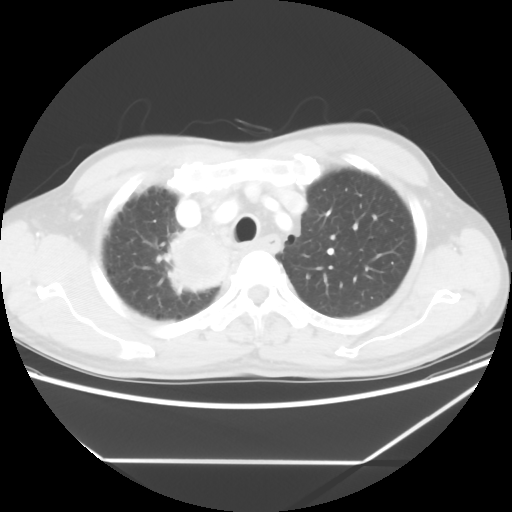
Chest CT, one axial slice; position 49 of 60 along the scan axis; reconstruction kernel STANDARD; 120 kVp; lung window (W 1500 / L -600 HU); 5 mm slice thickness; 512 × 512 image matrix, field of view 367 × 367 mm. Male patient, age 58 years. From the clinical record (not read from this slice): clinical TNM (as recorded): T2 N2 M0.
Annotated regions visible in this slice (rectangle marked by the reading radiologist):
- lung tumour (recorded histology: squamous cell carcinoma): bounding box <158,225,231,293> (left, top, right, bottom; pixels)